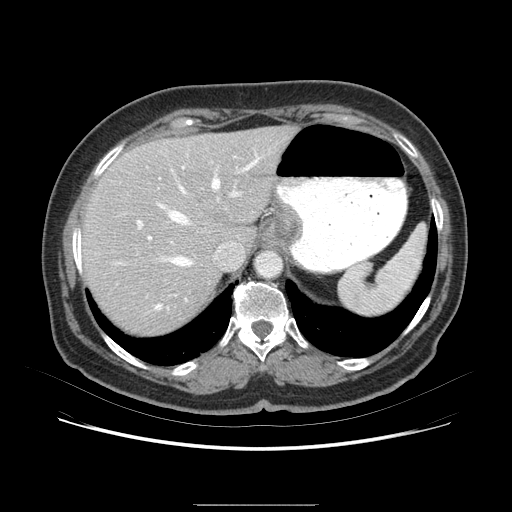
Contrast-enhanced abdominal CT (liver protocol), one axial slice; position 59 of 79 along the scan axis; 120 kVp; soft-tissue window (W 400 / L 40 HU); 2.5 mm slice thickness; 512 × 512 image matrix, field of view 380 × 380 mm. From the clinical record (not read from this slice): diagnosis: hepatocellular carcinoma (patient treated with transarterial chemoembolisation; whether this scan precedes or follows treatment is not stated here); TNM stage (as recorded): Stage-I; Child-Pugh class: A; tumour nodularity: uninodular.
Outlined on this slice (semi-automatically segmented with operator editing):
- liver parenchyma outside the tumour (the mass and vessels are separate outlines, so this box may not span the whole liver): bounding box (x1, y1, x2, y2) in pixels: (82, 132, 302, 320)
- liver vessels: (122, 177, 253, 257)